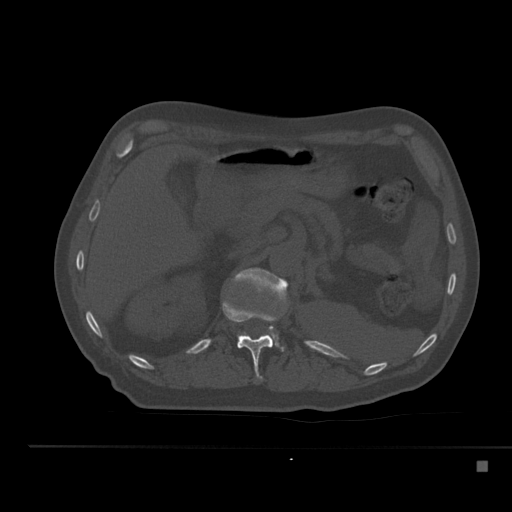
CT including the spine, one axial slice; slice 223 of 517 in the series (ordered by position); bone window (W 1800 / L 400 HU); 512 × 512 image matrix, field of view 408 × 408 mm. Patient: male, 70 years. From the clinical record (not read from this slice): primary cancer: renal; vertebrae with lytic lesions (as recorded): T4, T6, T10, T12, L3, L4, L5.
Outlined on this slice (semi-automatically segmented with operator editing):
- L1 vertebra: bounding box (x1, y1, x2, y2) in pixels: (233, 267, 288, 351)
- T12 vertebra: (222, 300, 282, 379)